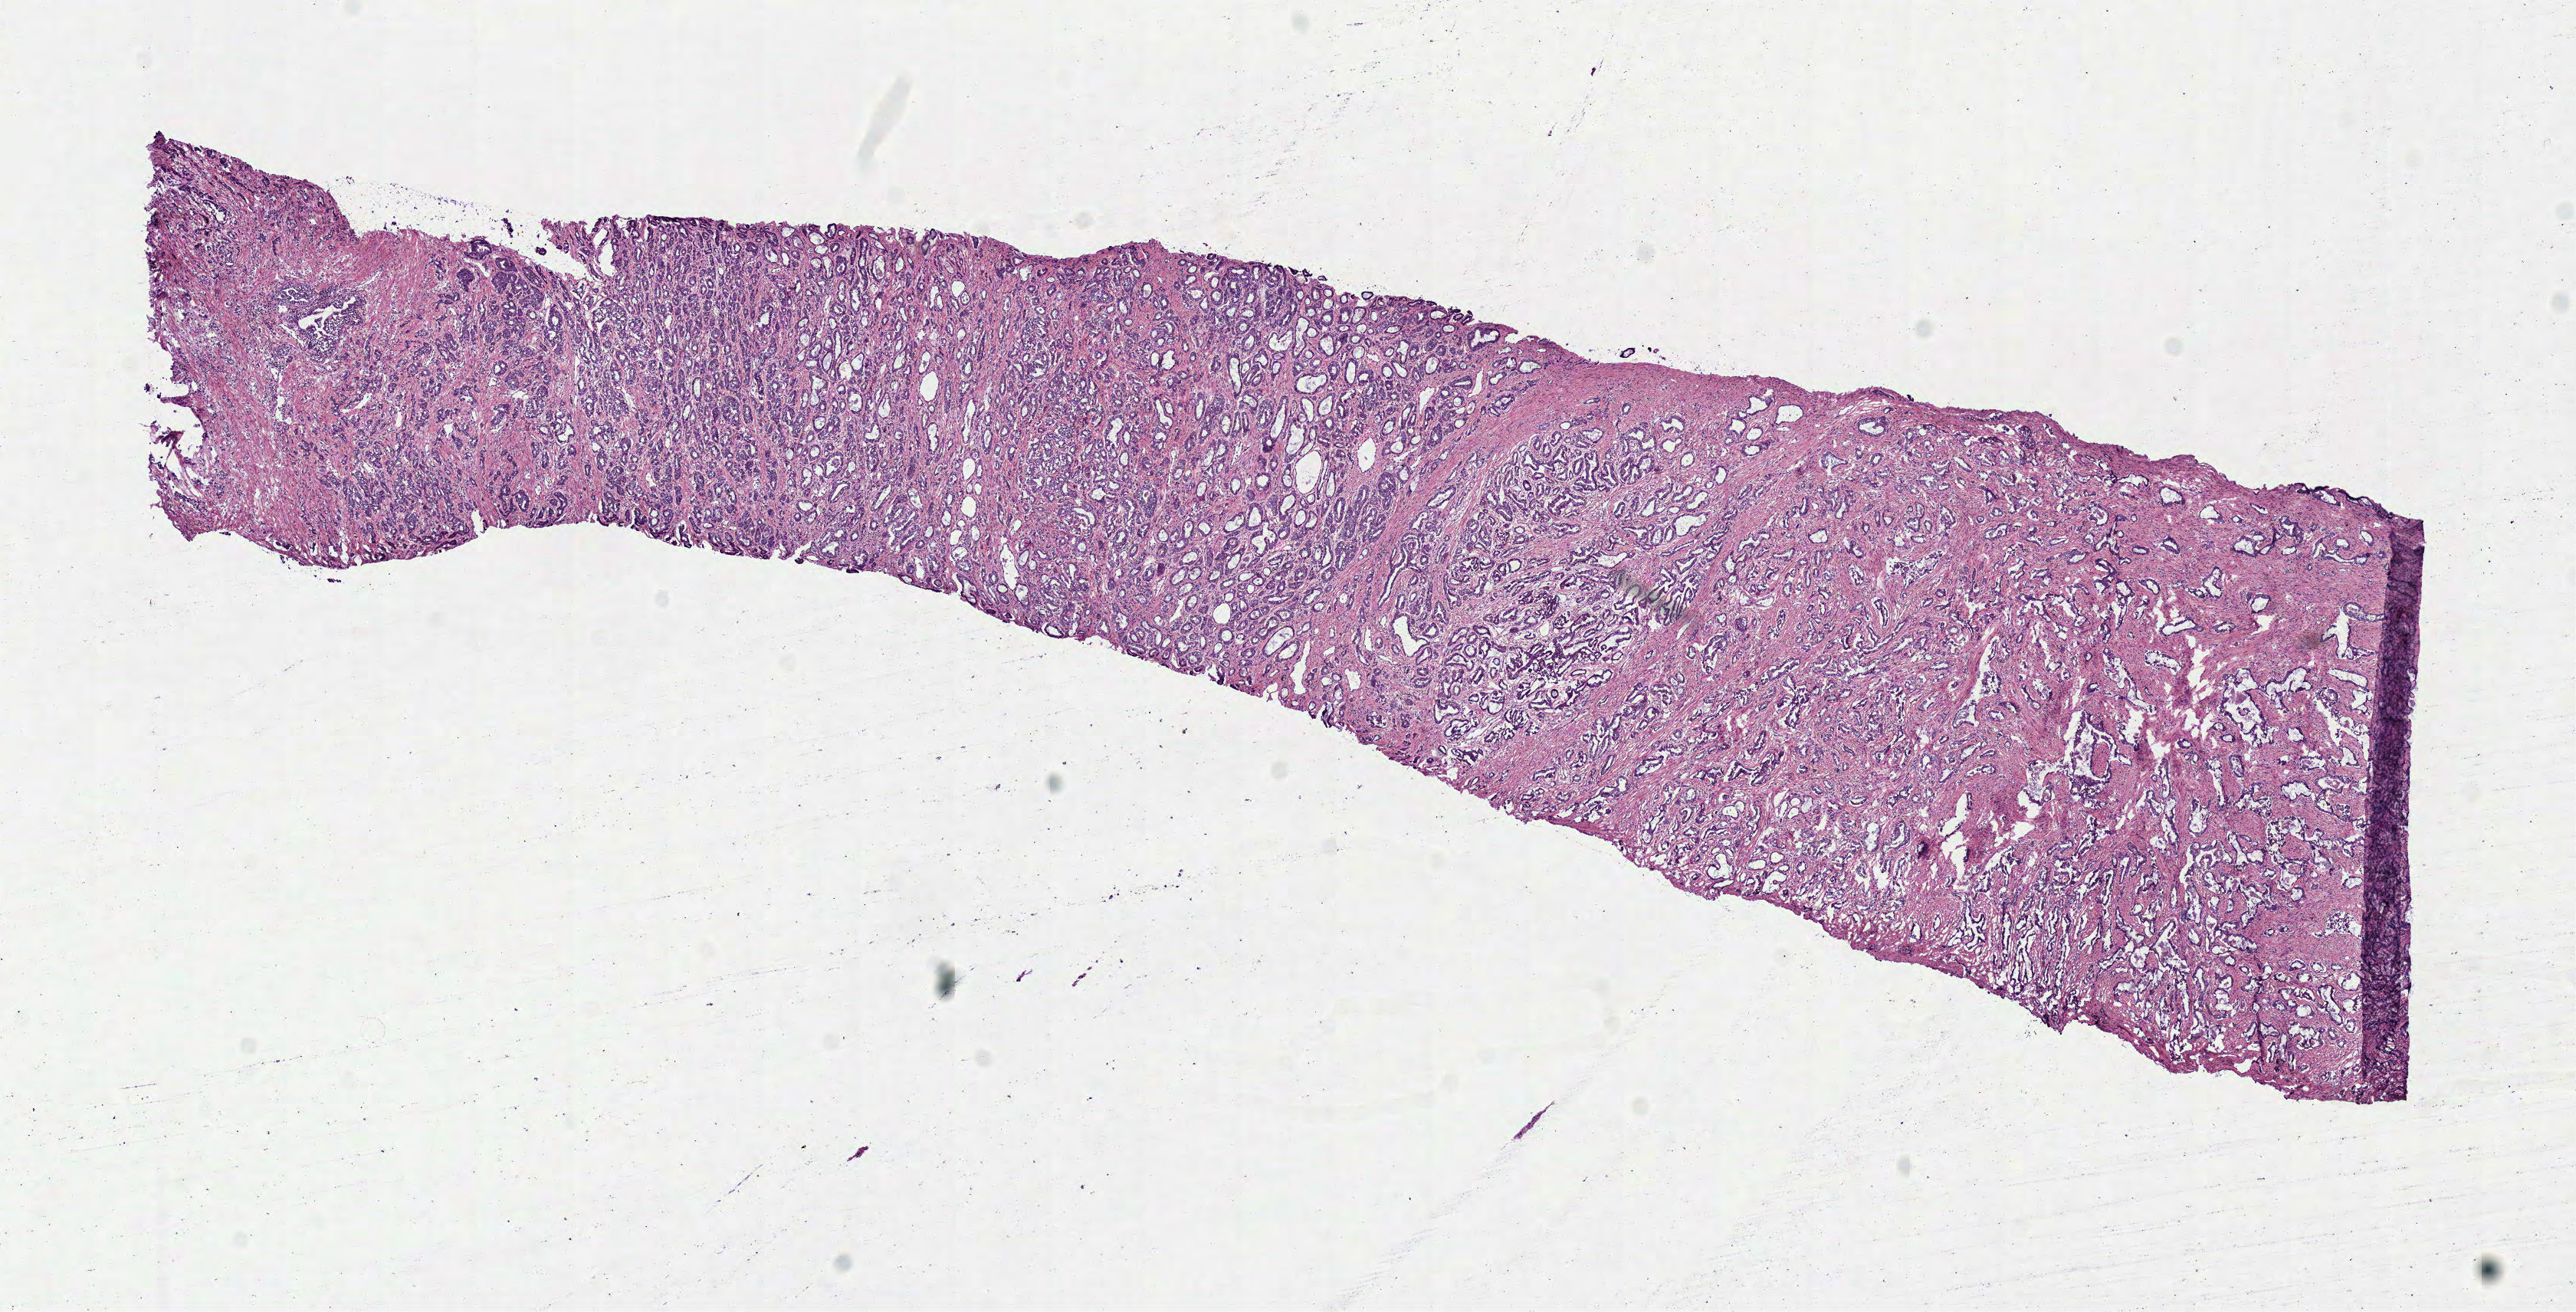
Hematoxylin and eosin (H&E) stained whole-slide image — whole scanned area (about 13.2 x 6.7 mm) shown as a low-resolution overview. Frozen section. Sample: primary tumour, prostate. Male patient; age at initial diagnosis 71 years. Gleason score: 7 (3+4). Slide review estimates, as recorded: tumour cells 75%, tumour nuclei 80%, normal cells 10%, stromal cells 15%, necrosis 0%. Infiltration values recorded for this section: lymphocyte infiltration 2%, monocyte infiltration 0%, neutrophil infiltration 0%.
* laterality: bilateral
* diagnosis: Acinar cell carcinoma (prostate gland)